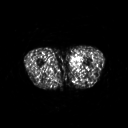
FDG PET of an extremity soft-tissue mass (from a PET/CT study), one axial slice. Slice 235 of 311 in the series (ordered by position). 128 × 128 image matrix, field of view 500 × 500 mm. Male patient, age 29 years. Case-level facts recorded for this patient, not image findings: histological type: mixoid liposarcoma; grade: low; site of the primary tumour: left thigh.
Outlined on this slice (expert contour drawn on MRI and transferred to this co-registered scan by the dataset authors):
- gross tumour volume (mass): bounding box [x1, y1, x2, y2] px = [71, 54, 82, 69]